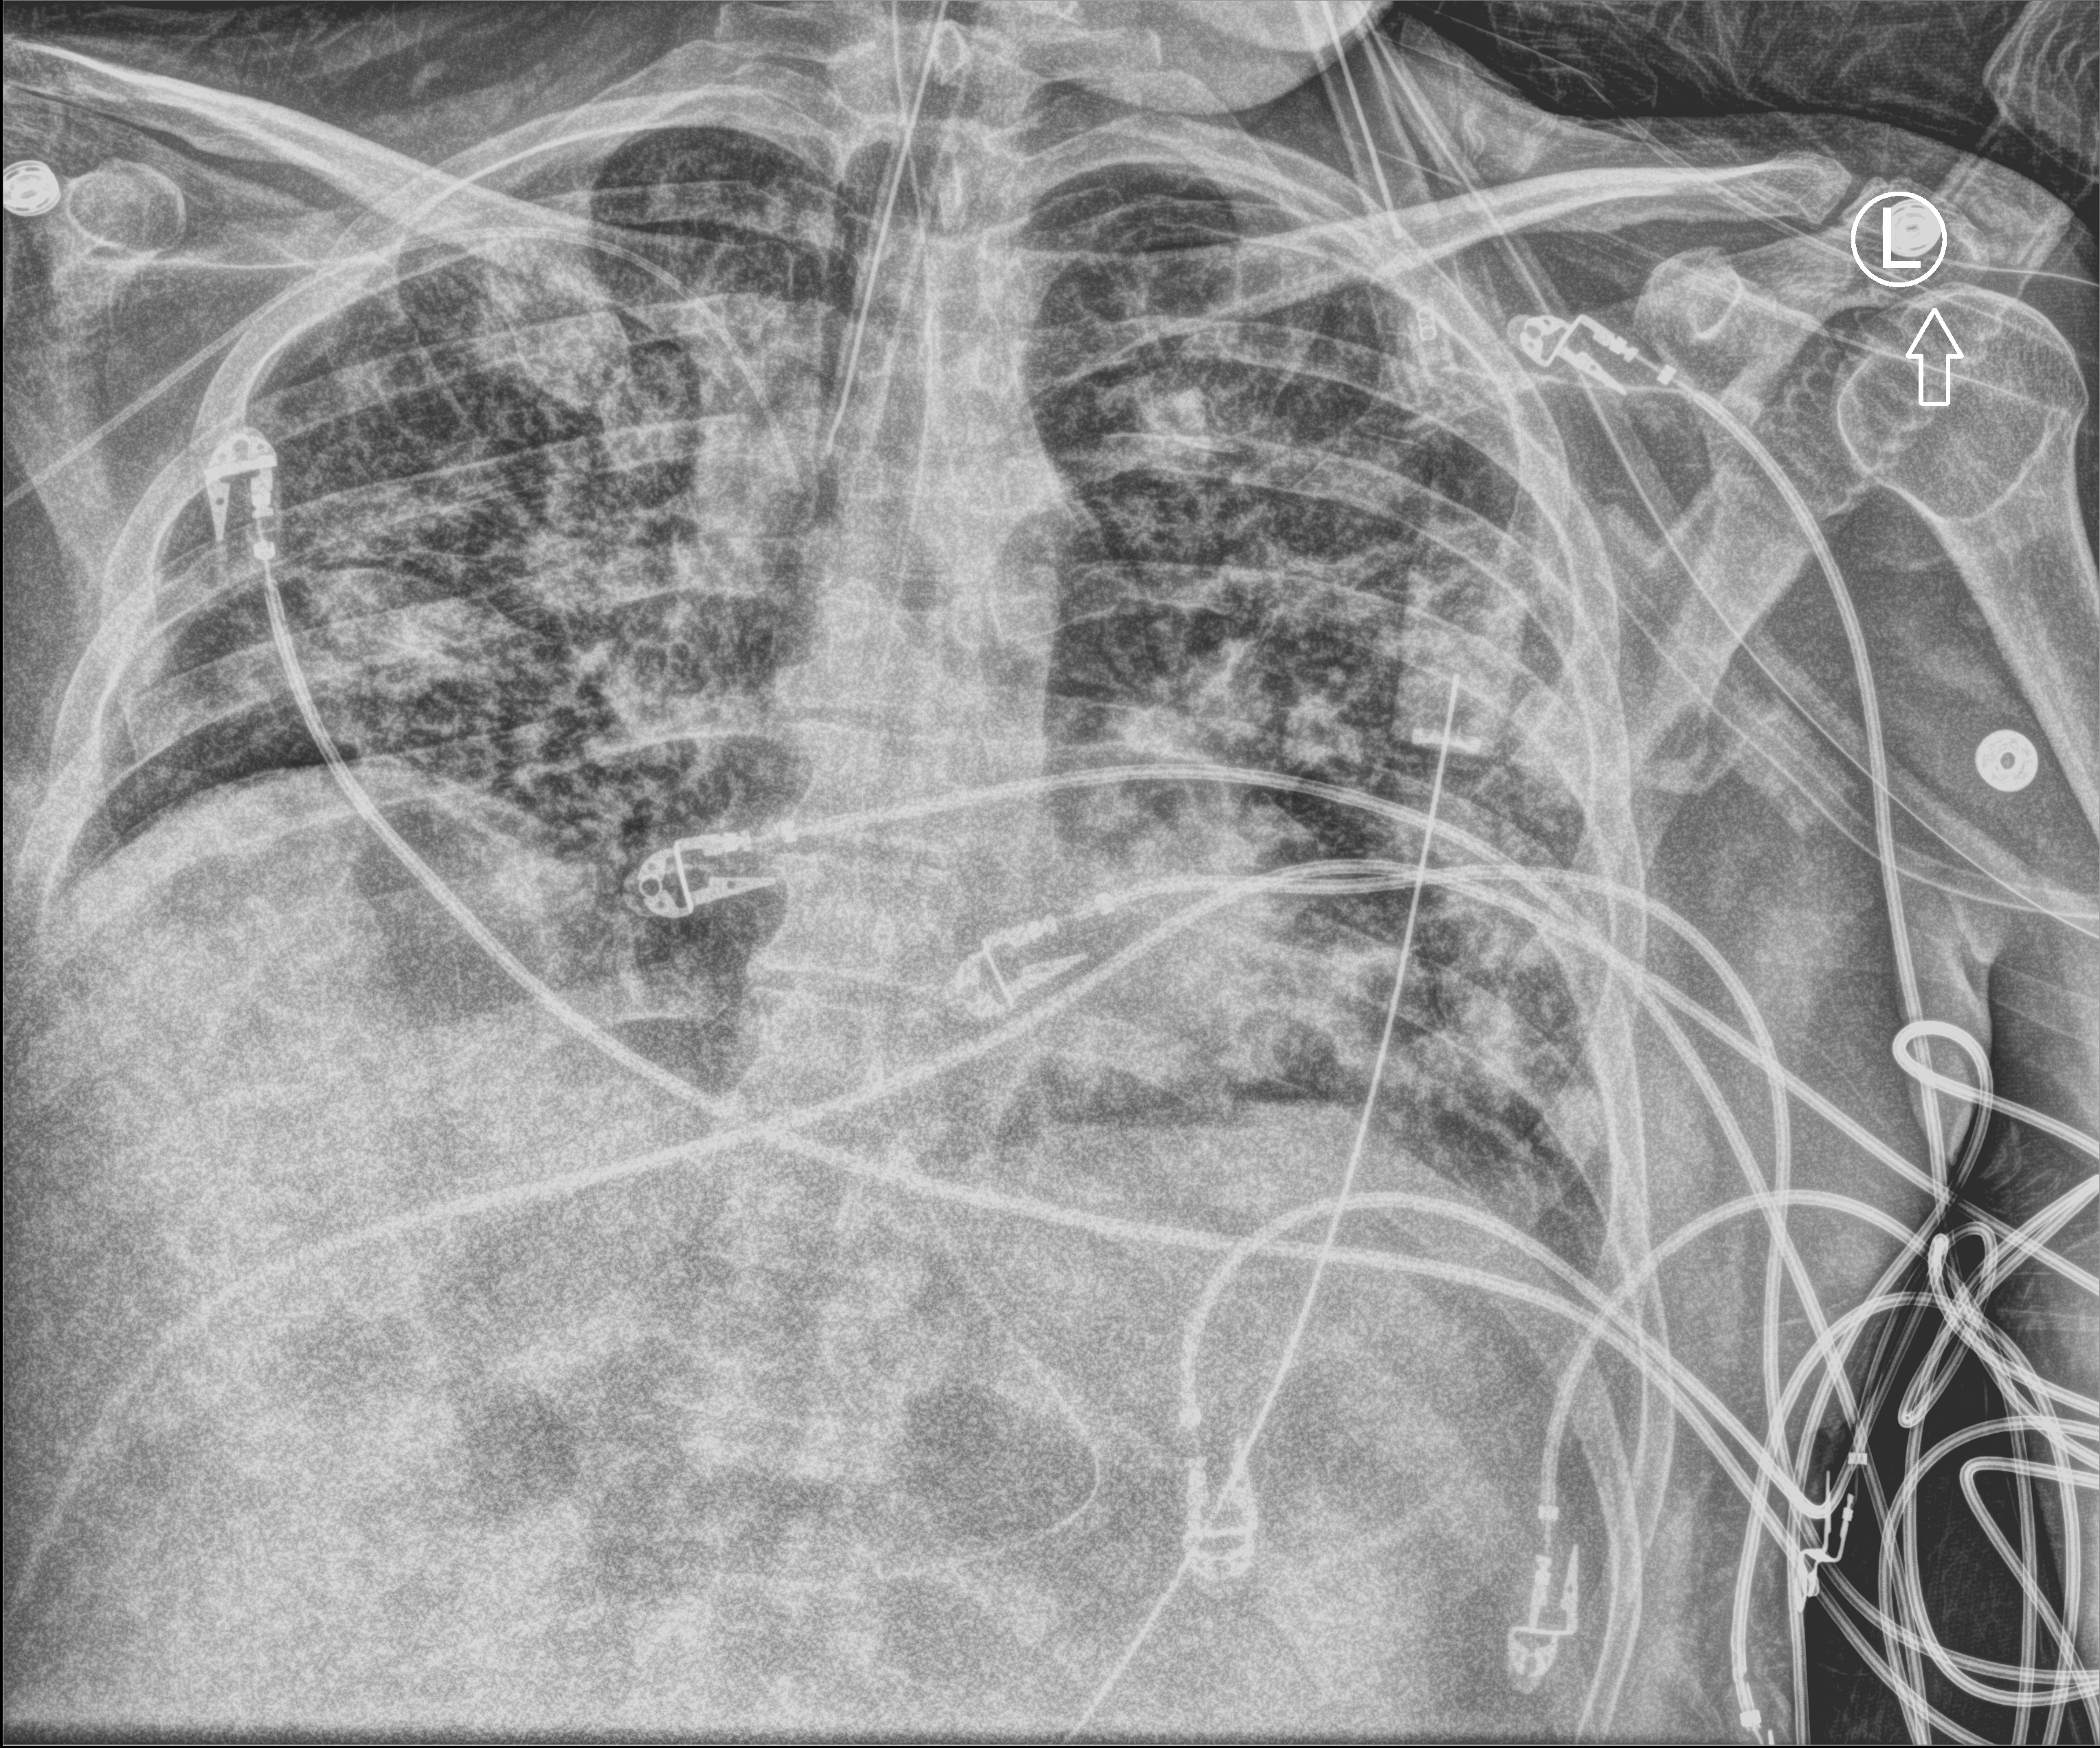
Chest X-ray (portable), anteroposterior (AP) projection. Patient hospitalised with COVID-19; male, aged 18–59 years.
Hospital-stay facts (about this admission, not read from this image; timing relative to this image not recorded): admitted to intensive care during this hospital stay: yes.